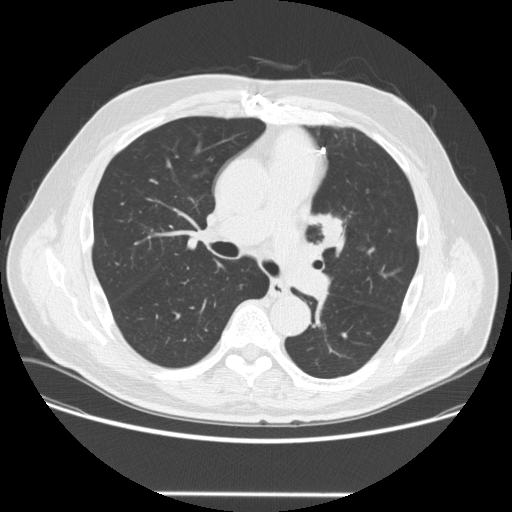
Low-dose screening chest CT, one axial slice. Slice 159 of 253 in the series (ordered by position). 120 kVp. Lung window (W 1500 / L -600 HU). 2.5 mm slice thickness. 512 × 512 image matrix, field of view 400 × 400 mm.
Annotated regions visible in this slice (expert manual segmentation):
- lesion 1 (tumor, upper lobe of left lung): bounding box [x1, y1, x2, y2] px = [320, 218, 343, 245]